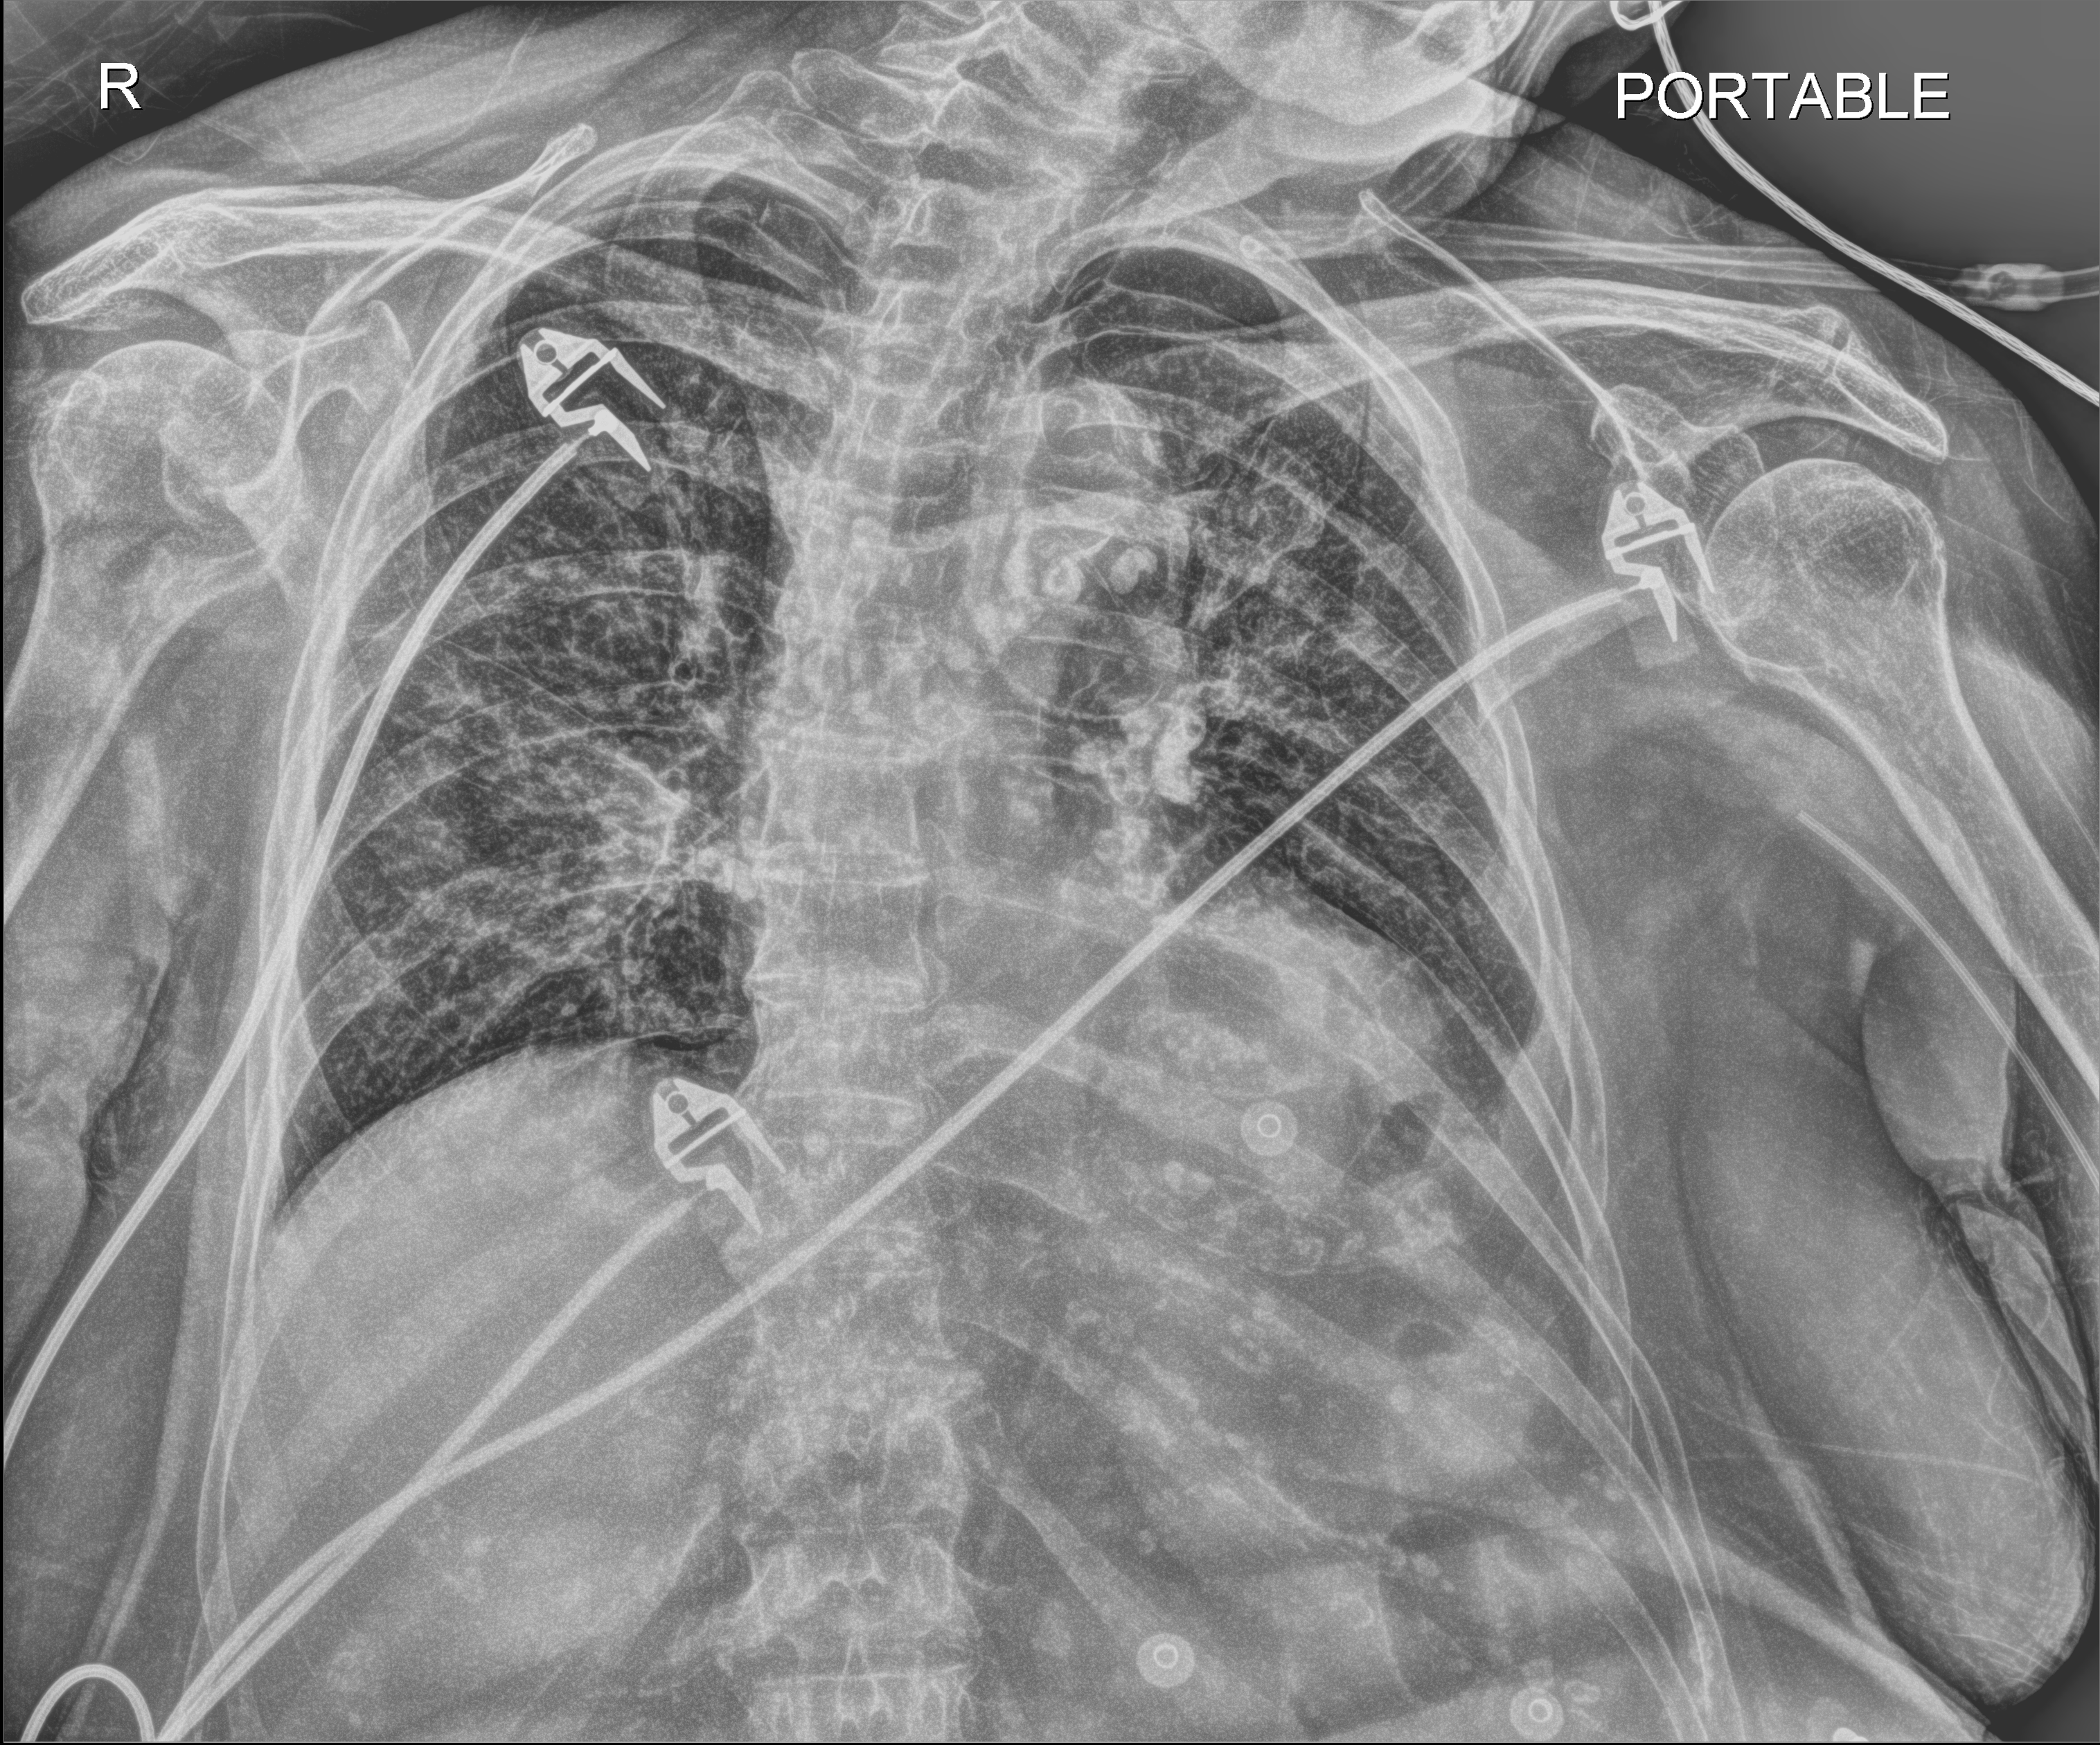
Chest X-ray (portable). Female patient hospitalised with COVID-19, age 75–90 years.
Hospital-stay facts (about this admission, not read from this image; timing relative to this image not recorded):
- mechanically ventilated during this hospital stay: no